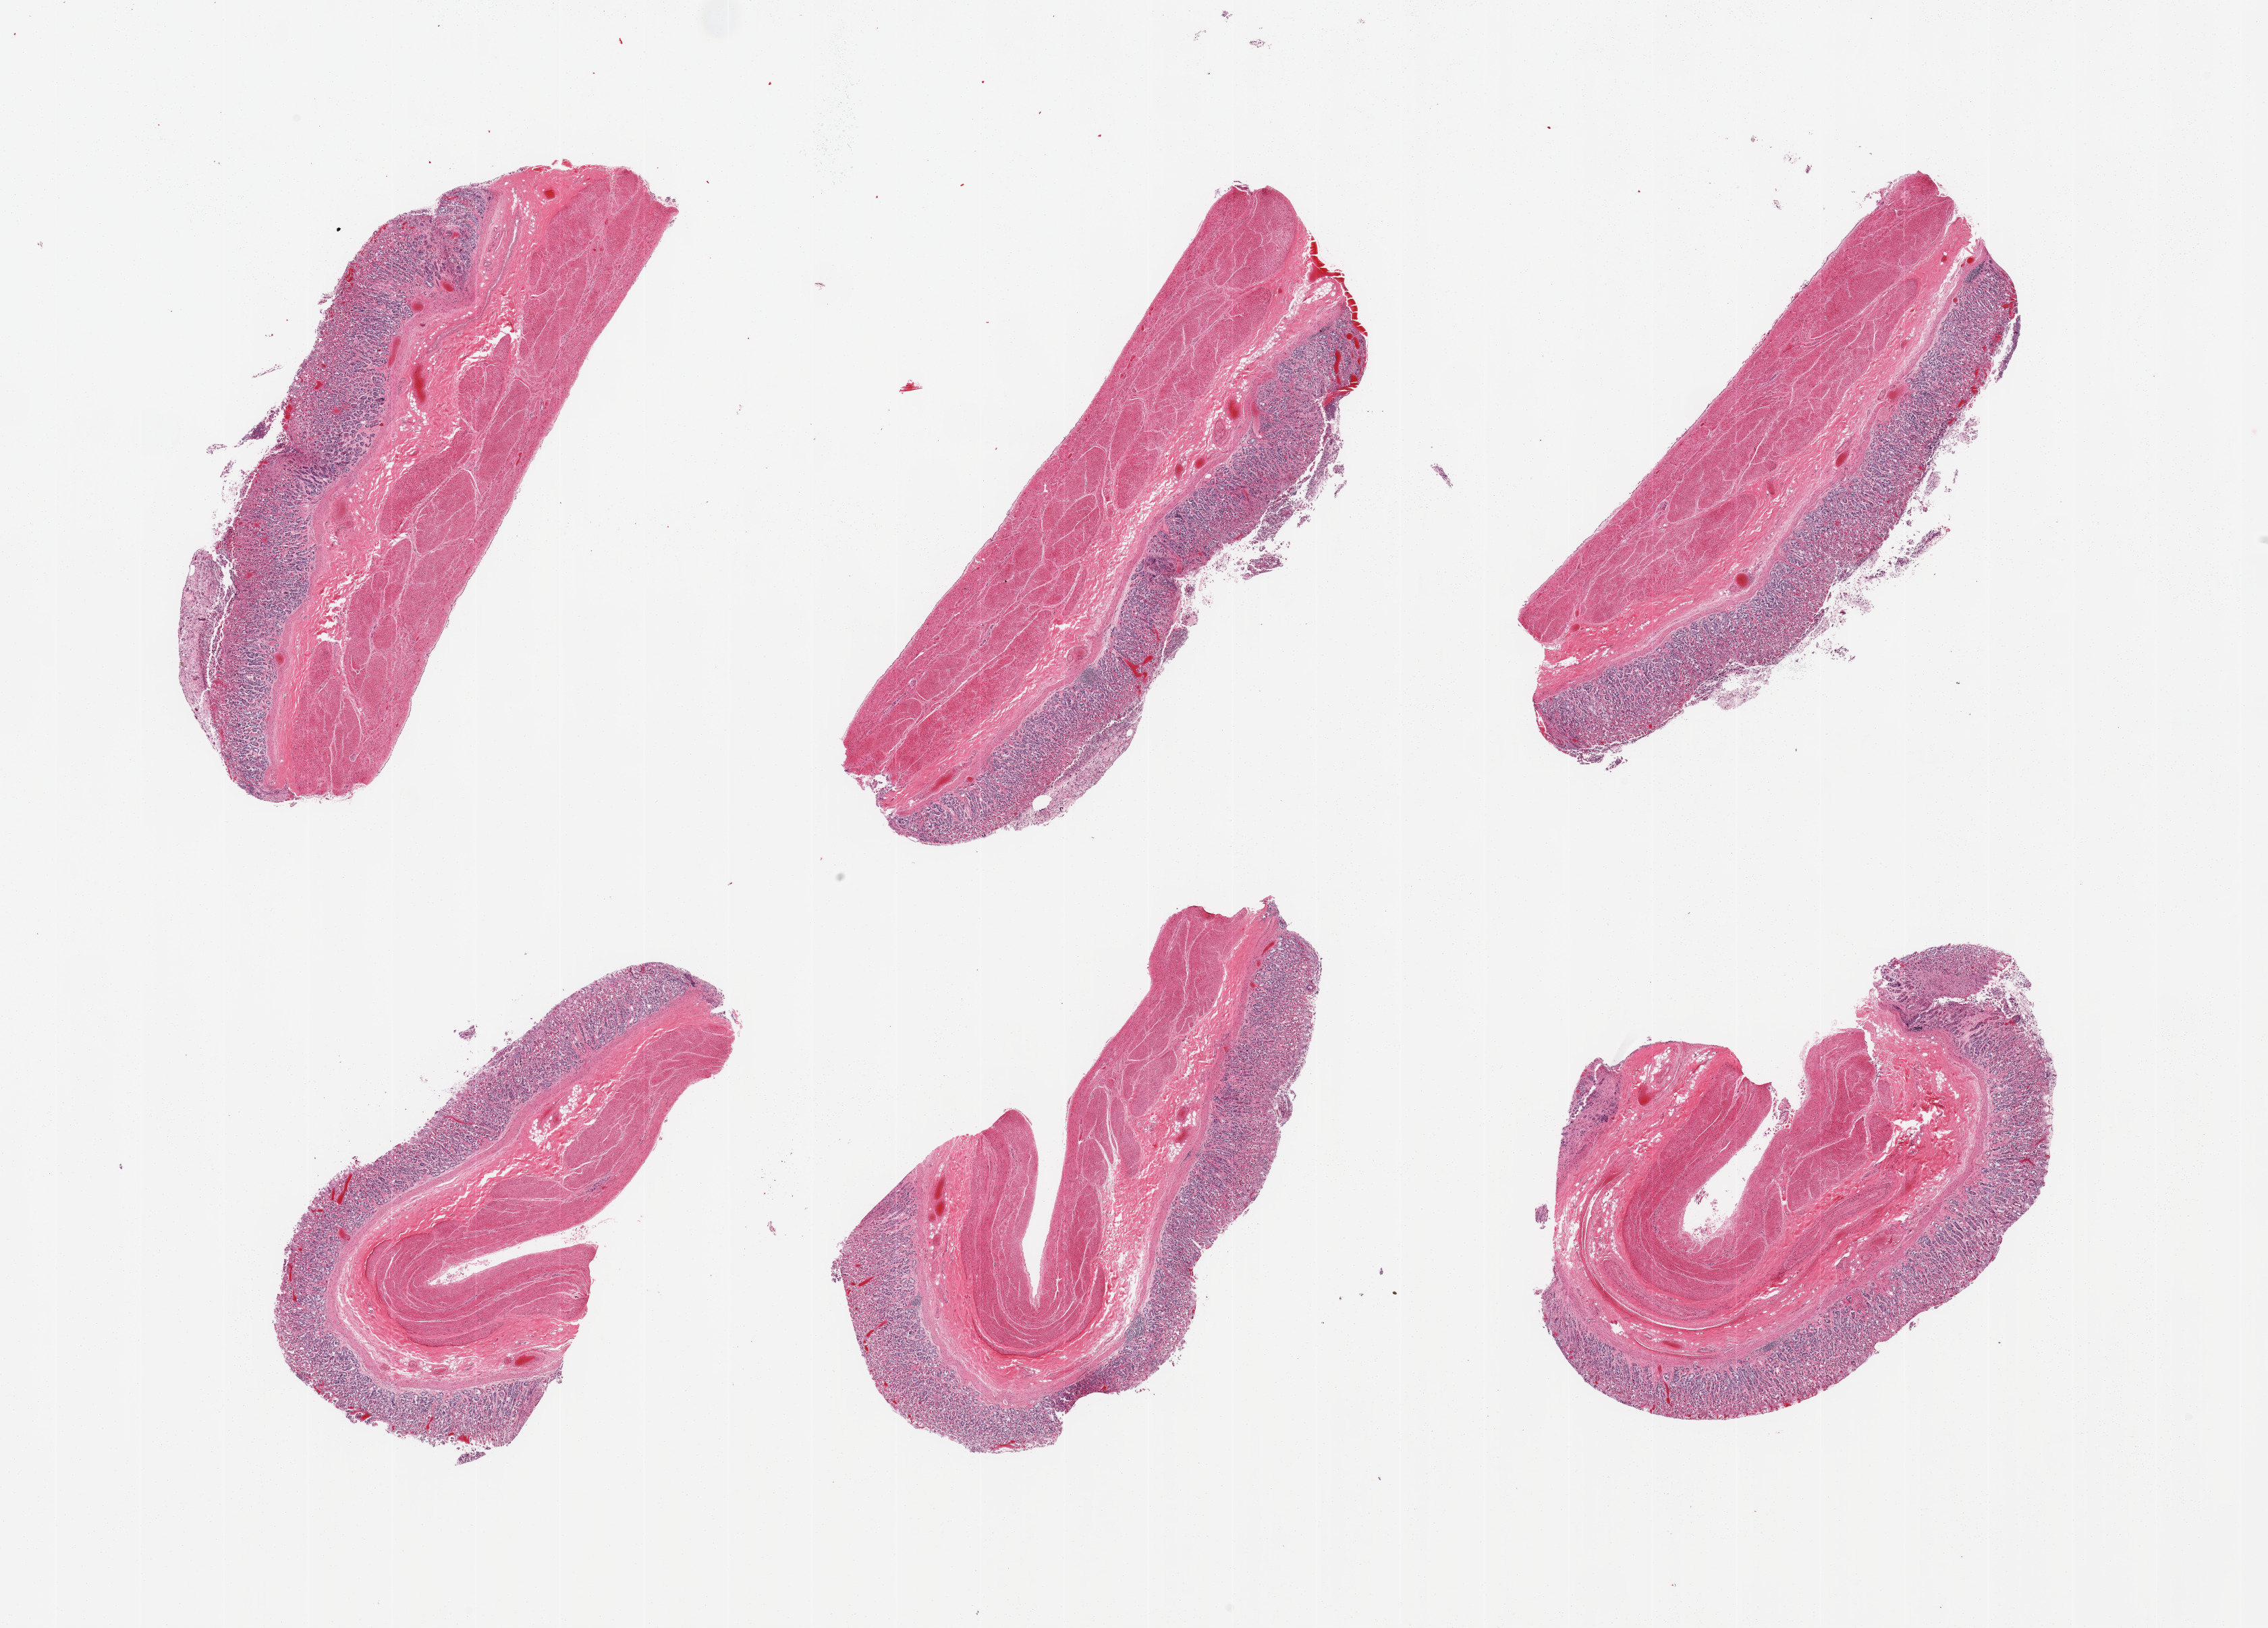
H&E whole-slide image — shown as a low-resolution overview of the whole scanned area (about 26.6 x 19.1 mm). PAXgene-fixed paraffin-embedded (PFPE) section. Section of stomach (target tissue). Donor tissue sample. Donor: male.
• reviewer comment on this tissue sample: 6 pieces; mildly to moderately autolyzed gastric mucosa; congestion; preserved muscularis